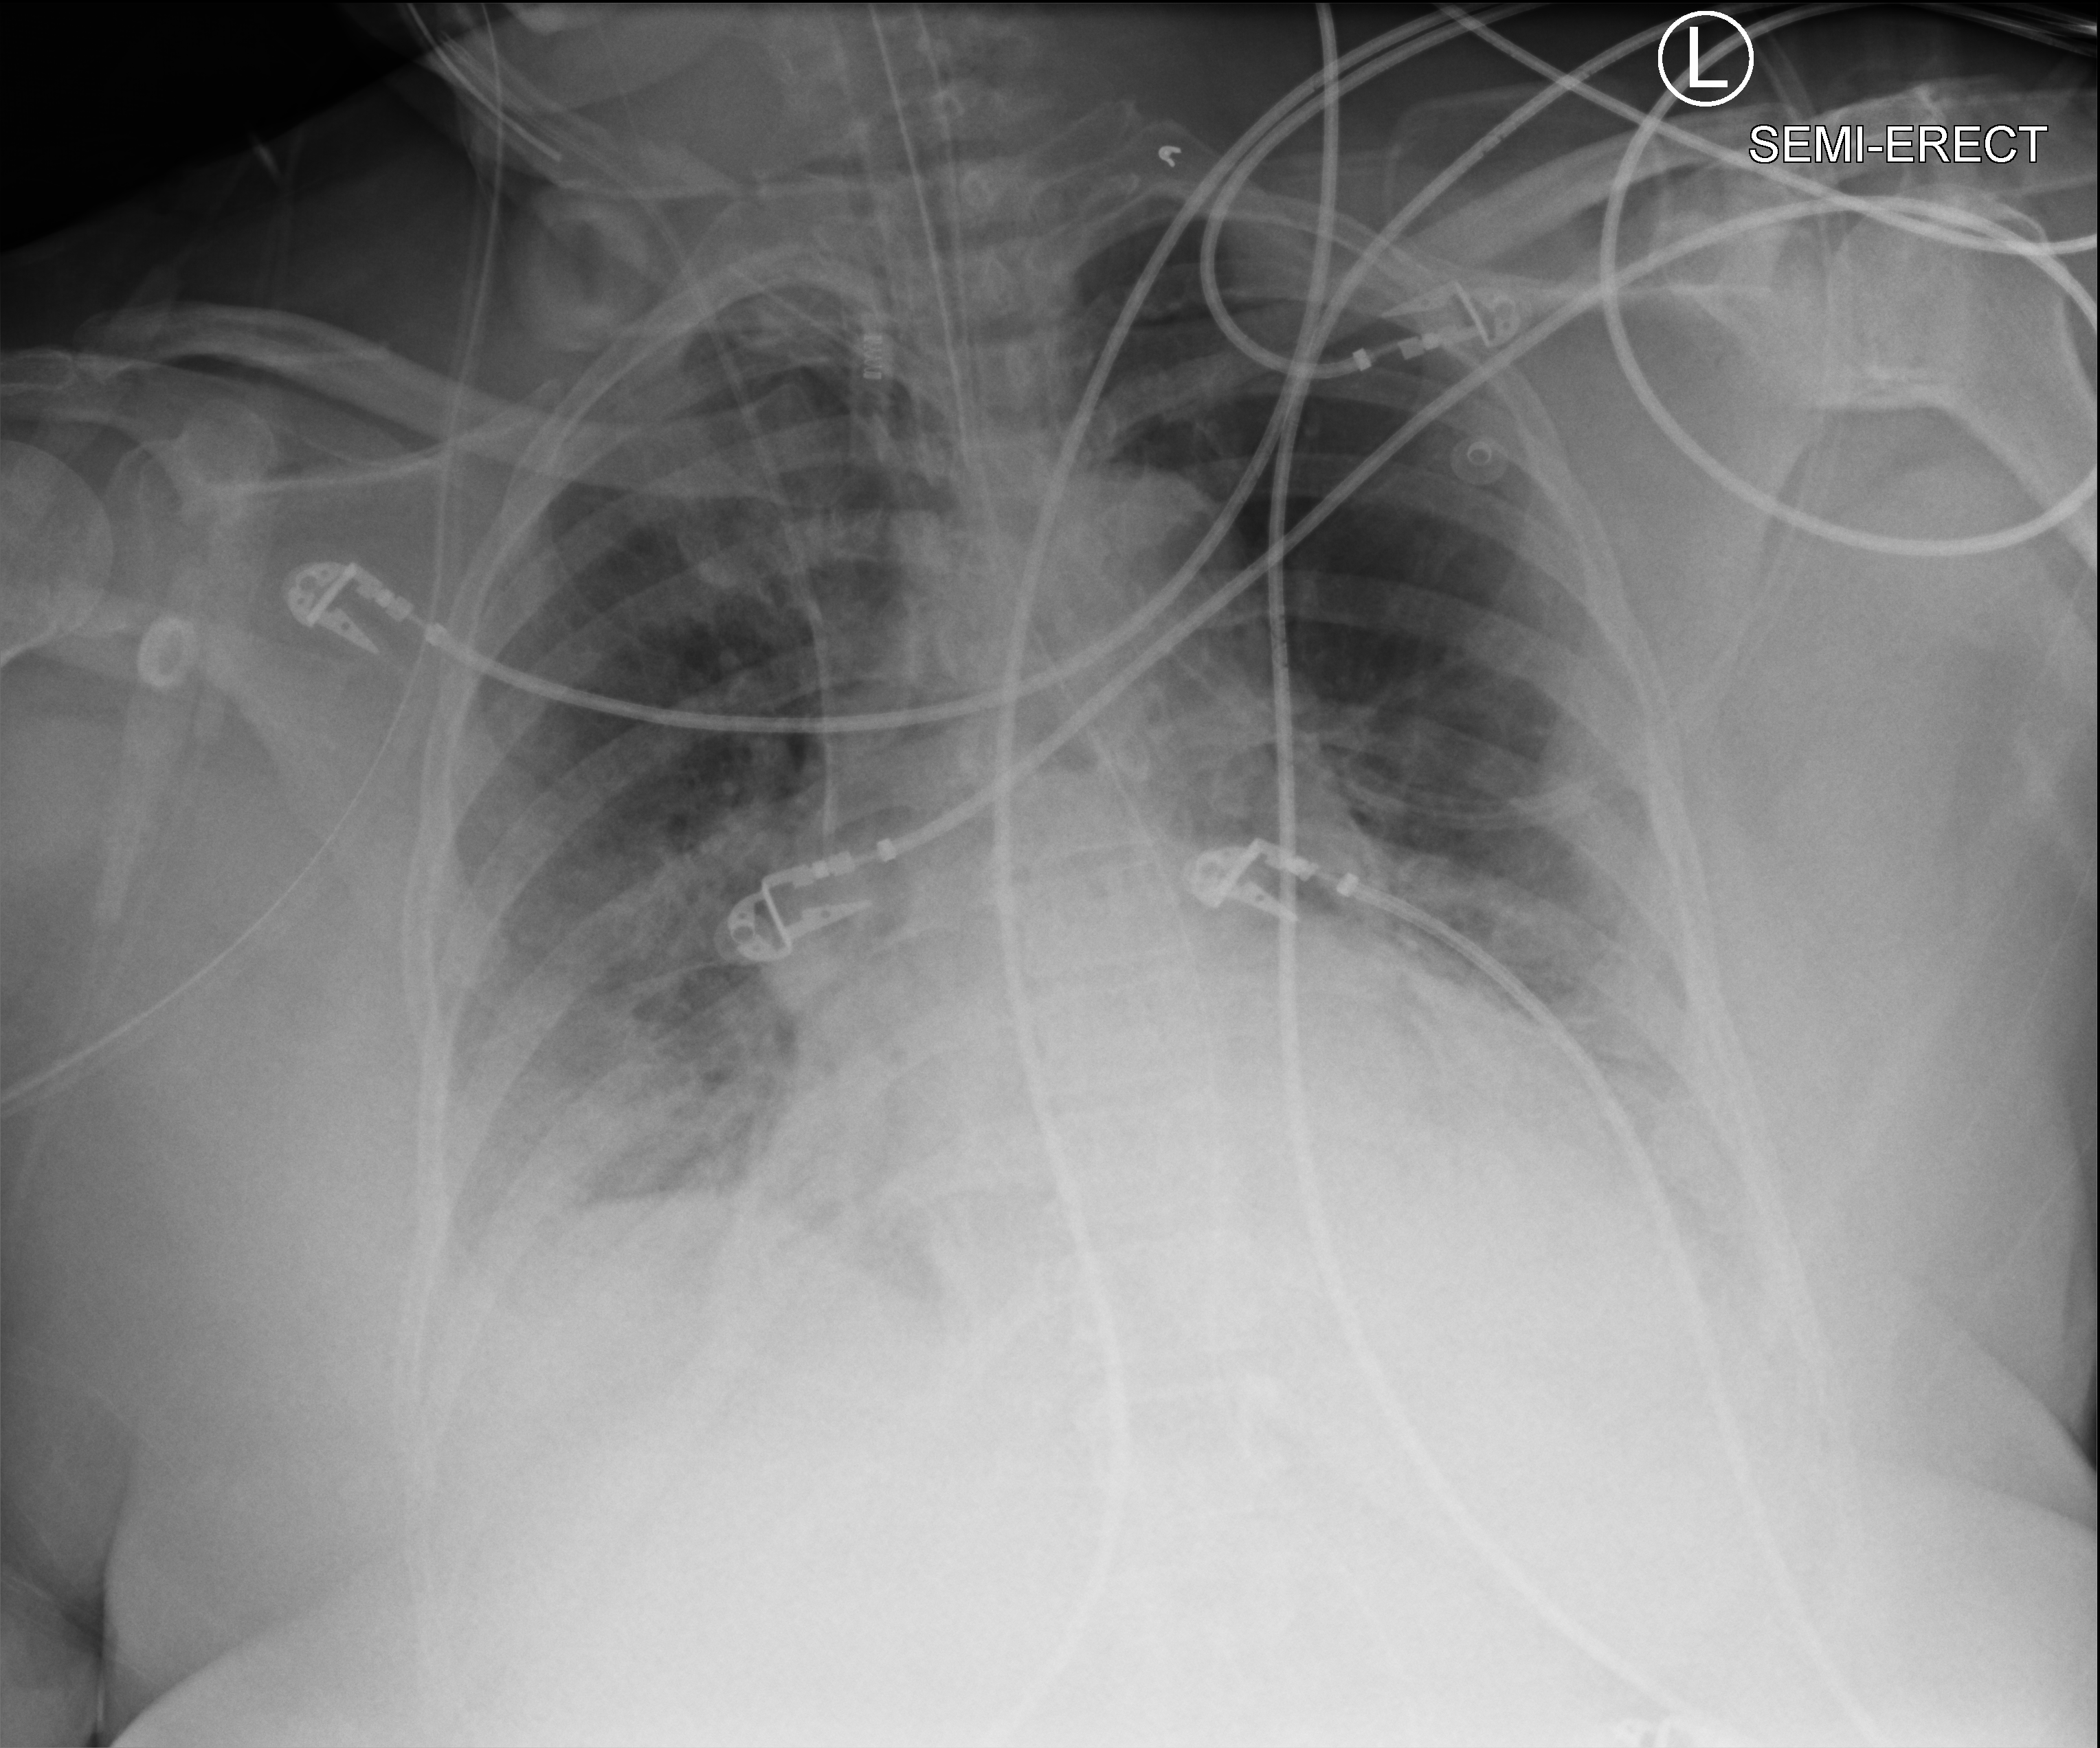
Portable chest radiograph; anteroposterior (AP) projection. Female patient hospitalised with COVID-19, age 60–74 years.
Hospital-stay facts (about this admission, not read from this image; timing relative to this image not recorded):
- mechanically ventilated during this hospital stay: yes
- COPD (admission record): no